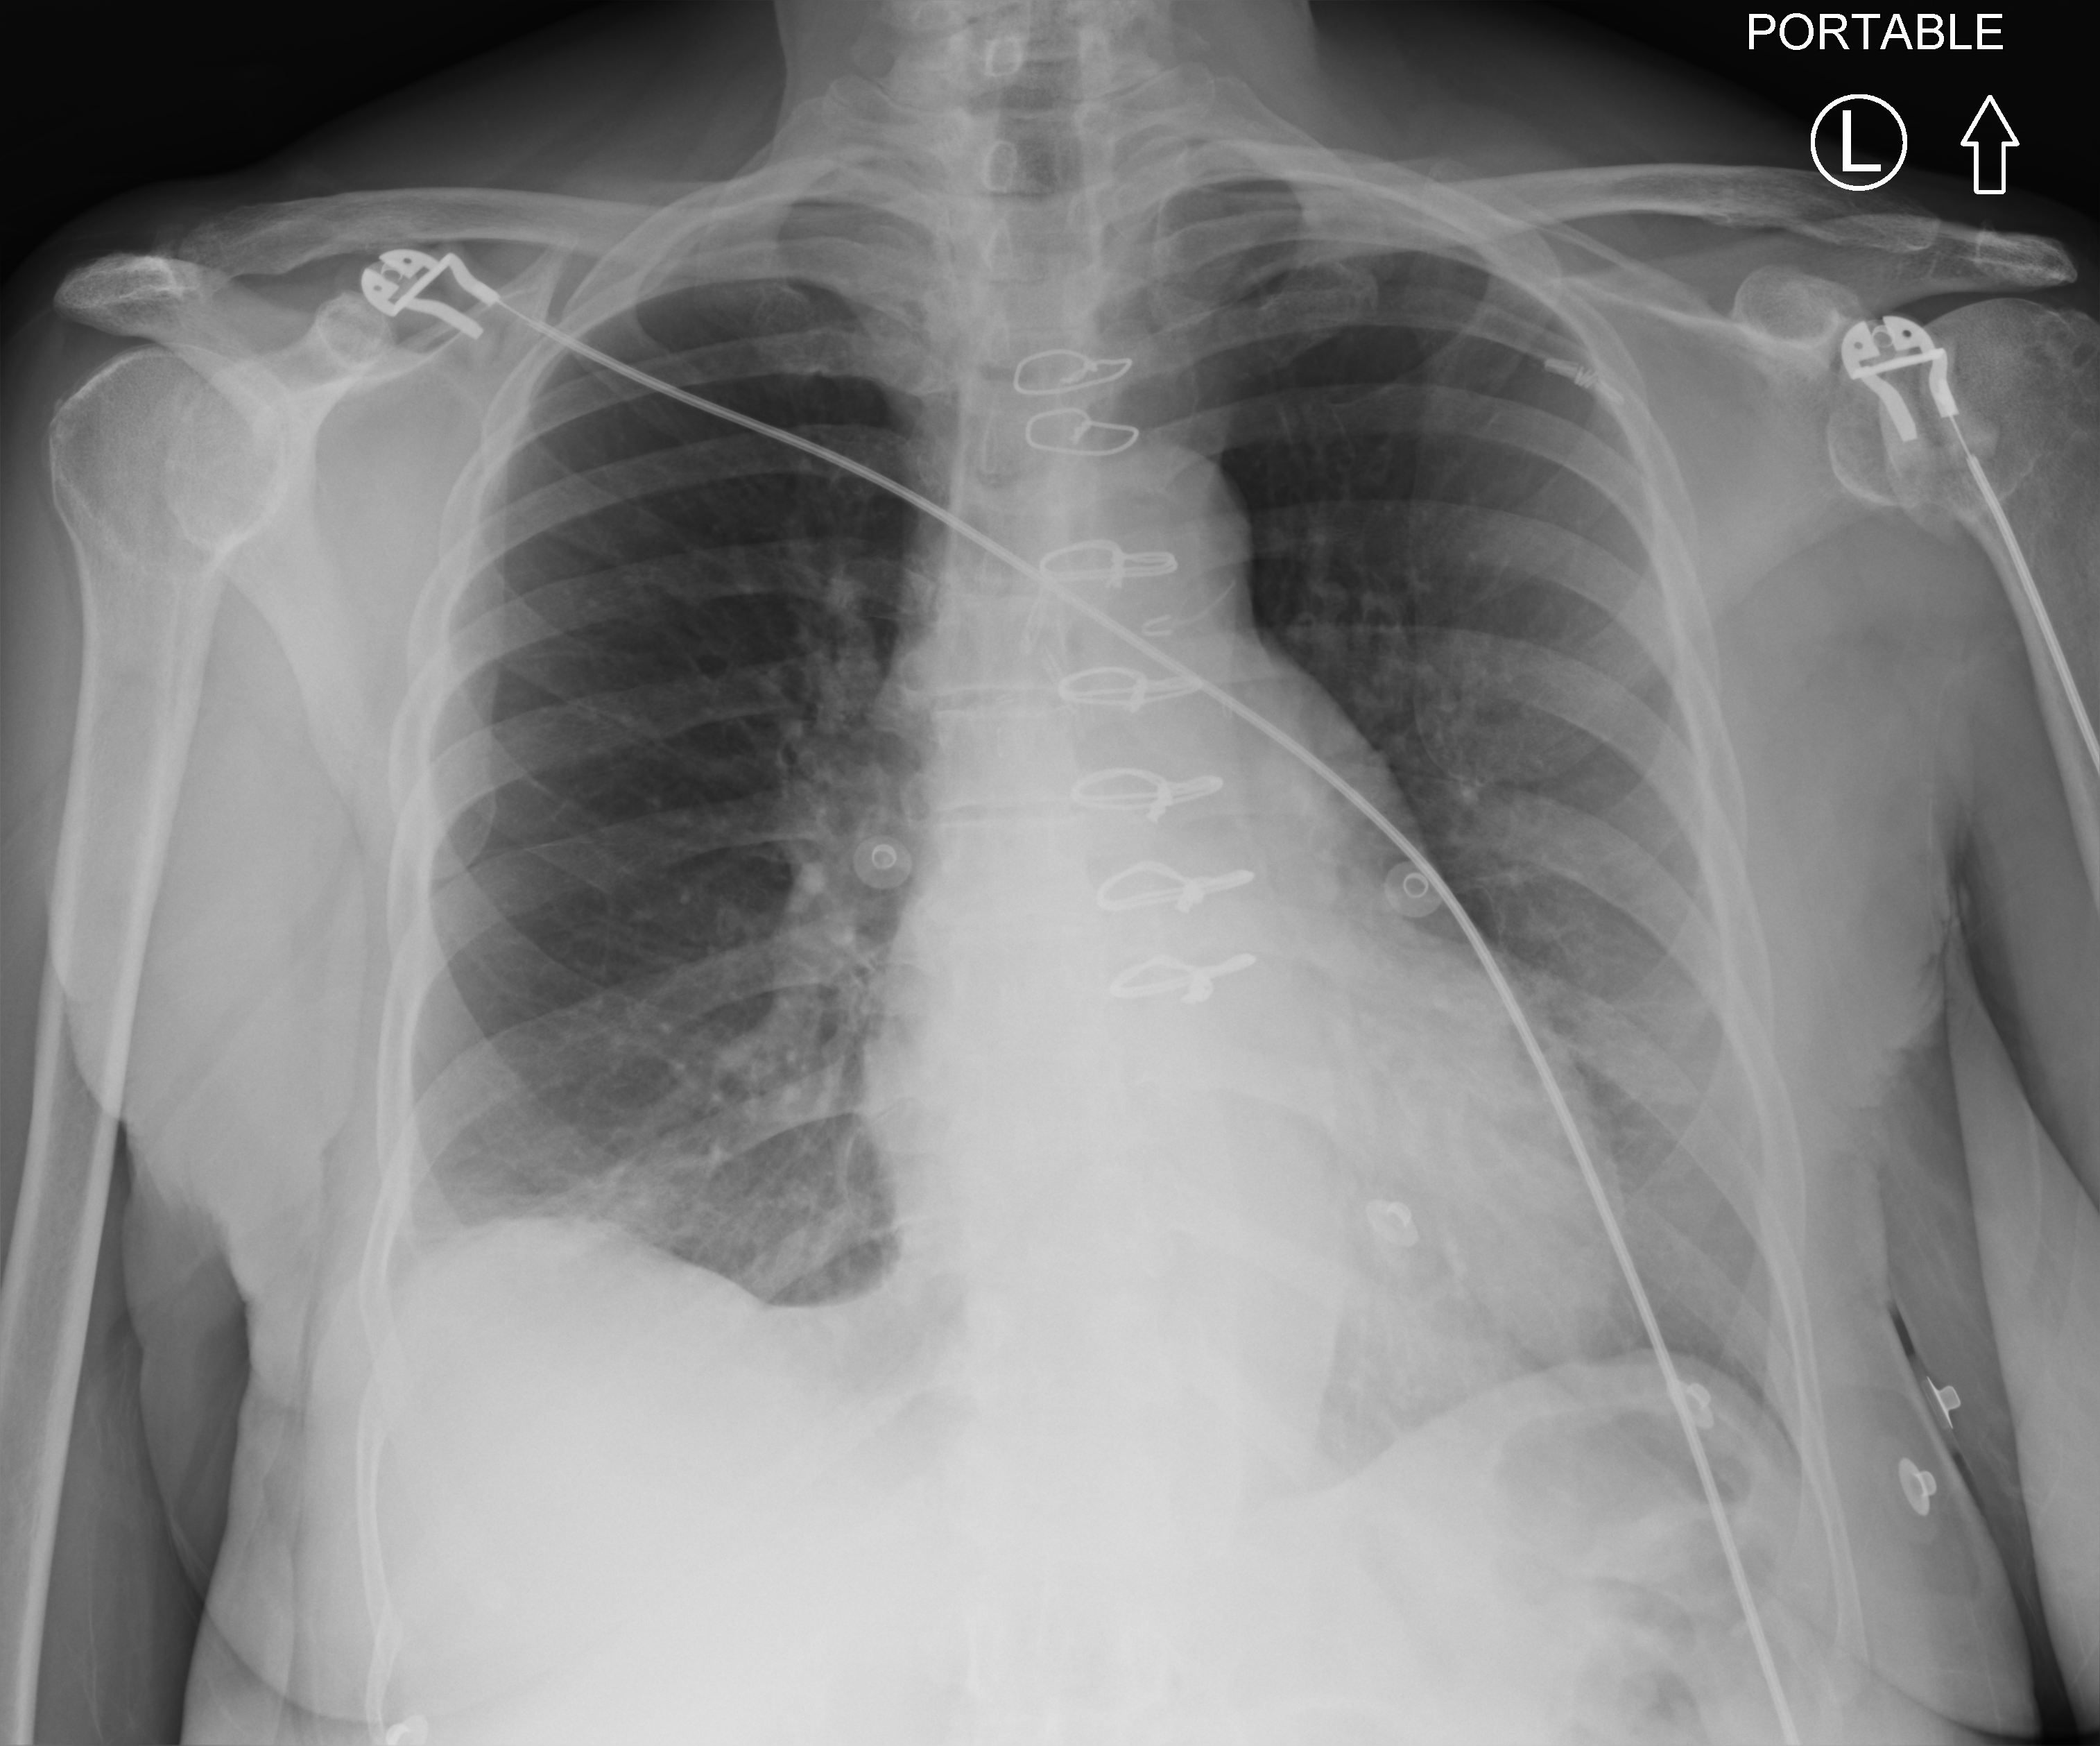
Chest X-ray (portable); anteroposterior (AP) projection. Patient hospitalised with COVID-19; female, aged 60–74 years.
Admission-level facts for this patient (not findings on this image; timing relative to this image not recorded): diabetes (admission record): yes; length of hospital stay: 3 days.